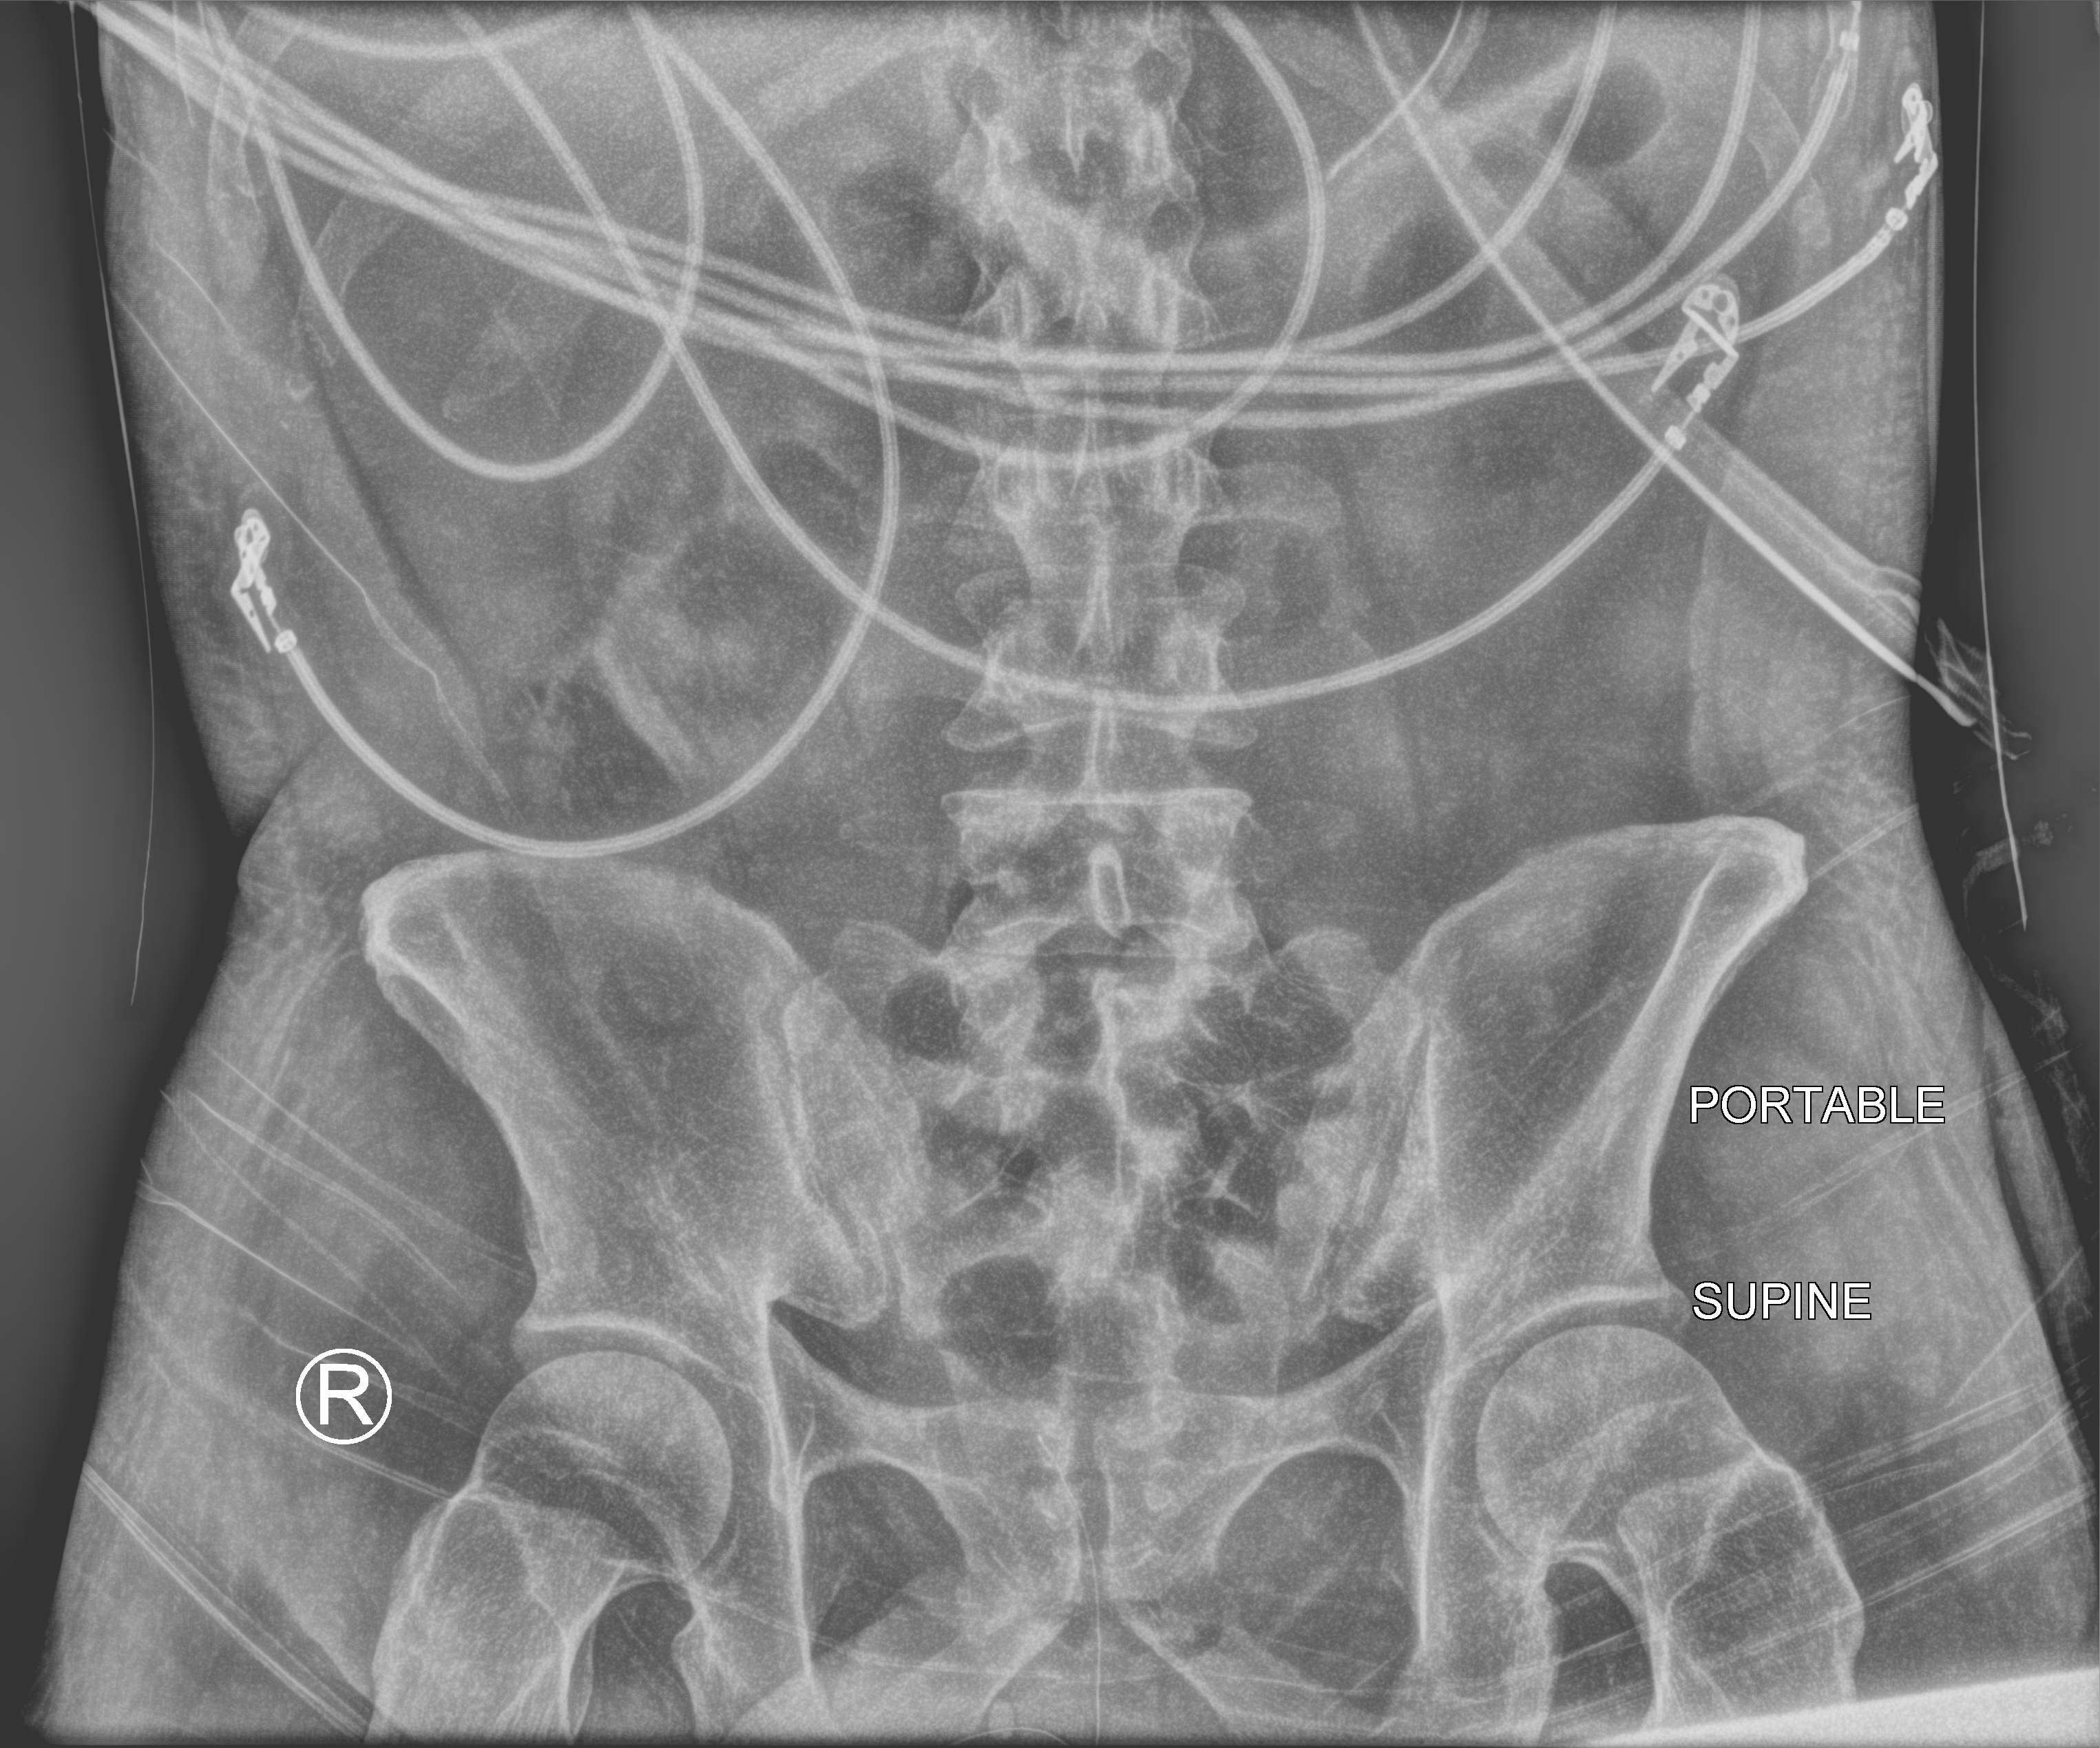
Abdomen X-ray (portable); anteroposterior (AP) projection. Male patient hospitalised with COVID-19, age 18–59 years.
Hospital-stay facts (about this admission, not read from this image; timing relative to this image not recorded):
- diabetes (admission record): yes
- mechanically ventilated during this hospital stay: yes
- admitted to intensive care during this hospital stay: yes